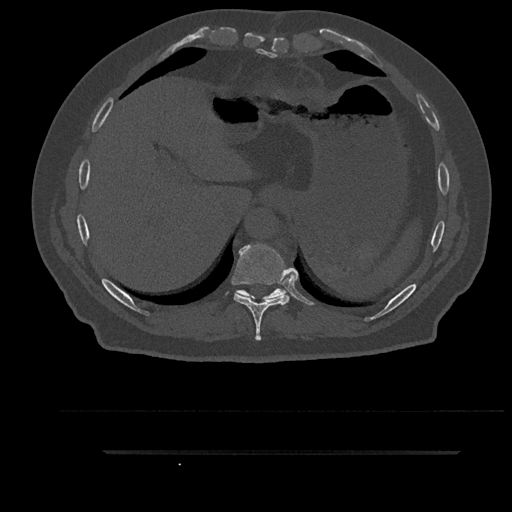
CT including the spine, one axial slice; slice 406 of 797 in the series (ordered by position); reconstruction kernel Br40s/3; bone window (W 1800 / L 400 HU); 512 × 512 image matrix. Patient: male, 63 years. Case-level facts recorded for this patient, not image findings: primary cancer: renal.
Annotated regions visible in this slice (semi-automatic segmentation, software-assisted and operator-edited):
- T10 vertebra: bounding box [x1, y1, x2, y2] px = [235, 289, 286, 299]
- T9 vertebra: [234, 244, 289, 341]